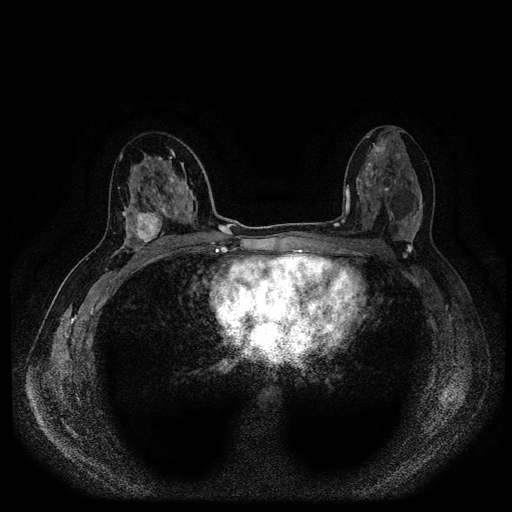
Breast MRI (dynamic contrast-enhanced, multi-phase), one axial slice. Slice 55 of 116 in the series (ordered by position). Dynamic contrast-enhanced series, time point 2 of 5 at this slice position (early post-contrast). 1.5 T. TE 2.6 ms, TR 5.4 ms. 2 mm slice thickness. 512 × 512 image matrix. Female patient, age 48 years.
Annotated regions visible in this slice (semi-automatic segmentation, software-assisted and operator-edited):
- breast lesion (labelled 'tumour' in the annotation; benign lesions carry a separate 'benign' label): bounding box [x1, y1, x2, y2] px = [132, 209, 165, 248]